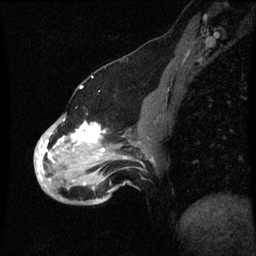
Breast MRI (dynamic contrast-enhanced), one sagittal slice; position 22 of 60 along the scan axis; dynamic contrast-enhanced series, image 2 of 3 at this slice position (ordered by acquisition); 1.5 T; TE 4.2 ms, TR 8.9 ms; 2 mm slice thickness; 256 × 256 image matrix, field of view 200 × 200 mm. Patient: female, 49 years. Case-level facts recorded for this patient, not image findings: setting: breast cancer imaged before/during neoadjuvant chemotherapy; receptor status: HR-positive, HER2-negative.
Outlined on this slice (semi-automatically segmented with operator editing):
- analysis volume of interest (the breast-tissue region the enhancement analysis was run in; not a lesion): bounding box (x1, y1, x2, y2) in pixels: (36, 114, 149, 199)
- tumour enhancement mask (voxels above the 70 % enhancement threshold inside the analysis volume of interest): (40, 122, 105, 179)